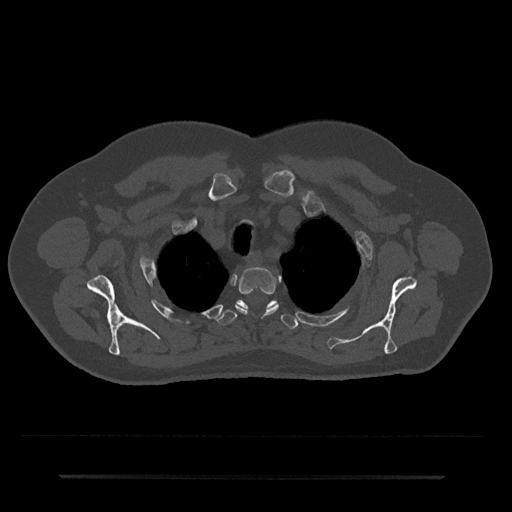
CT including the spine, one axial slice; slice 591 of 797 in the series (ordered by position); 120 kVp; bone window (W 1800 / L 400 HU); 0.5 mm slice thickness; 512 × 512 image matrix, field of view 437 × 437 mm. Patient: male, 69 years. Case-level facts recorded for this patient, not image findings: primary cancer: prostate.
Structures marked on this image (semi-automatic segmentation, software-assisted and operator-edited):
- T2 vertebra: bounding box <235,267,279,315> (left, top, right, bottom; pixels)
- T3 vertebra: <217,299,297,330>